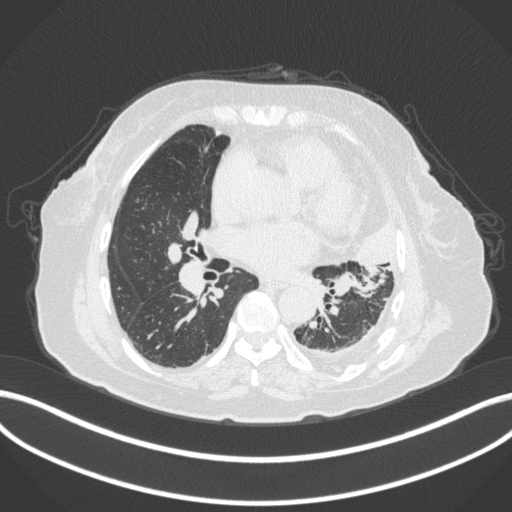
Chest CT, one axial slice. Position 177 of 399 along the scan axis. Reconstruction kernel B31f. Lung window (W 1500 / L -600 HU). 1 mm slice thickness. 512 × 512 image matrix, field of view 400 × 400 mm. Patient: female, 75 years. Case-level facts recorded for this patient, not image findings: clinical TNM (as recorded): T3 N3 M1.
Structures marked on this image (bounding box drawn by a radiologist):
- lung tumour (recorded histology: adenocarcinoma): bounding box <359,218,403,275> (left, top, right, bottom; pixels)